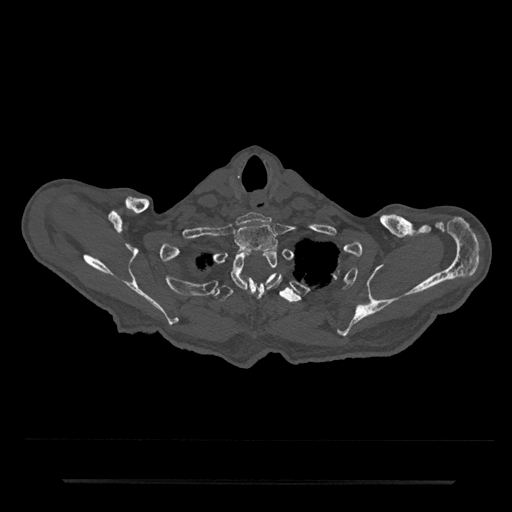
CT including the spine, one axial slice; 120 kVp; bone window (W 1800 / L 400 HU); 512 × 512 image matrix, field of view 427 × 427 mm. Patient: male, 74 years. From the clinical record (not read from this slice): primary cancer: prostate.
Structures marked on this image (semi-automatic segmentation, software-assisted and operator-edited):
- T1 vertebra: box from (x=234, y=223) to (x=279, y=253) px
- T2 vertebra: (x=231, y=250)–(x=282, y=300)
- T3 vertebra: (x=213, y=273)–(x=302, y=303)